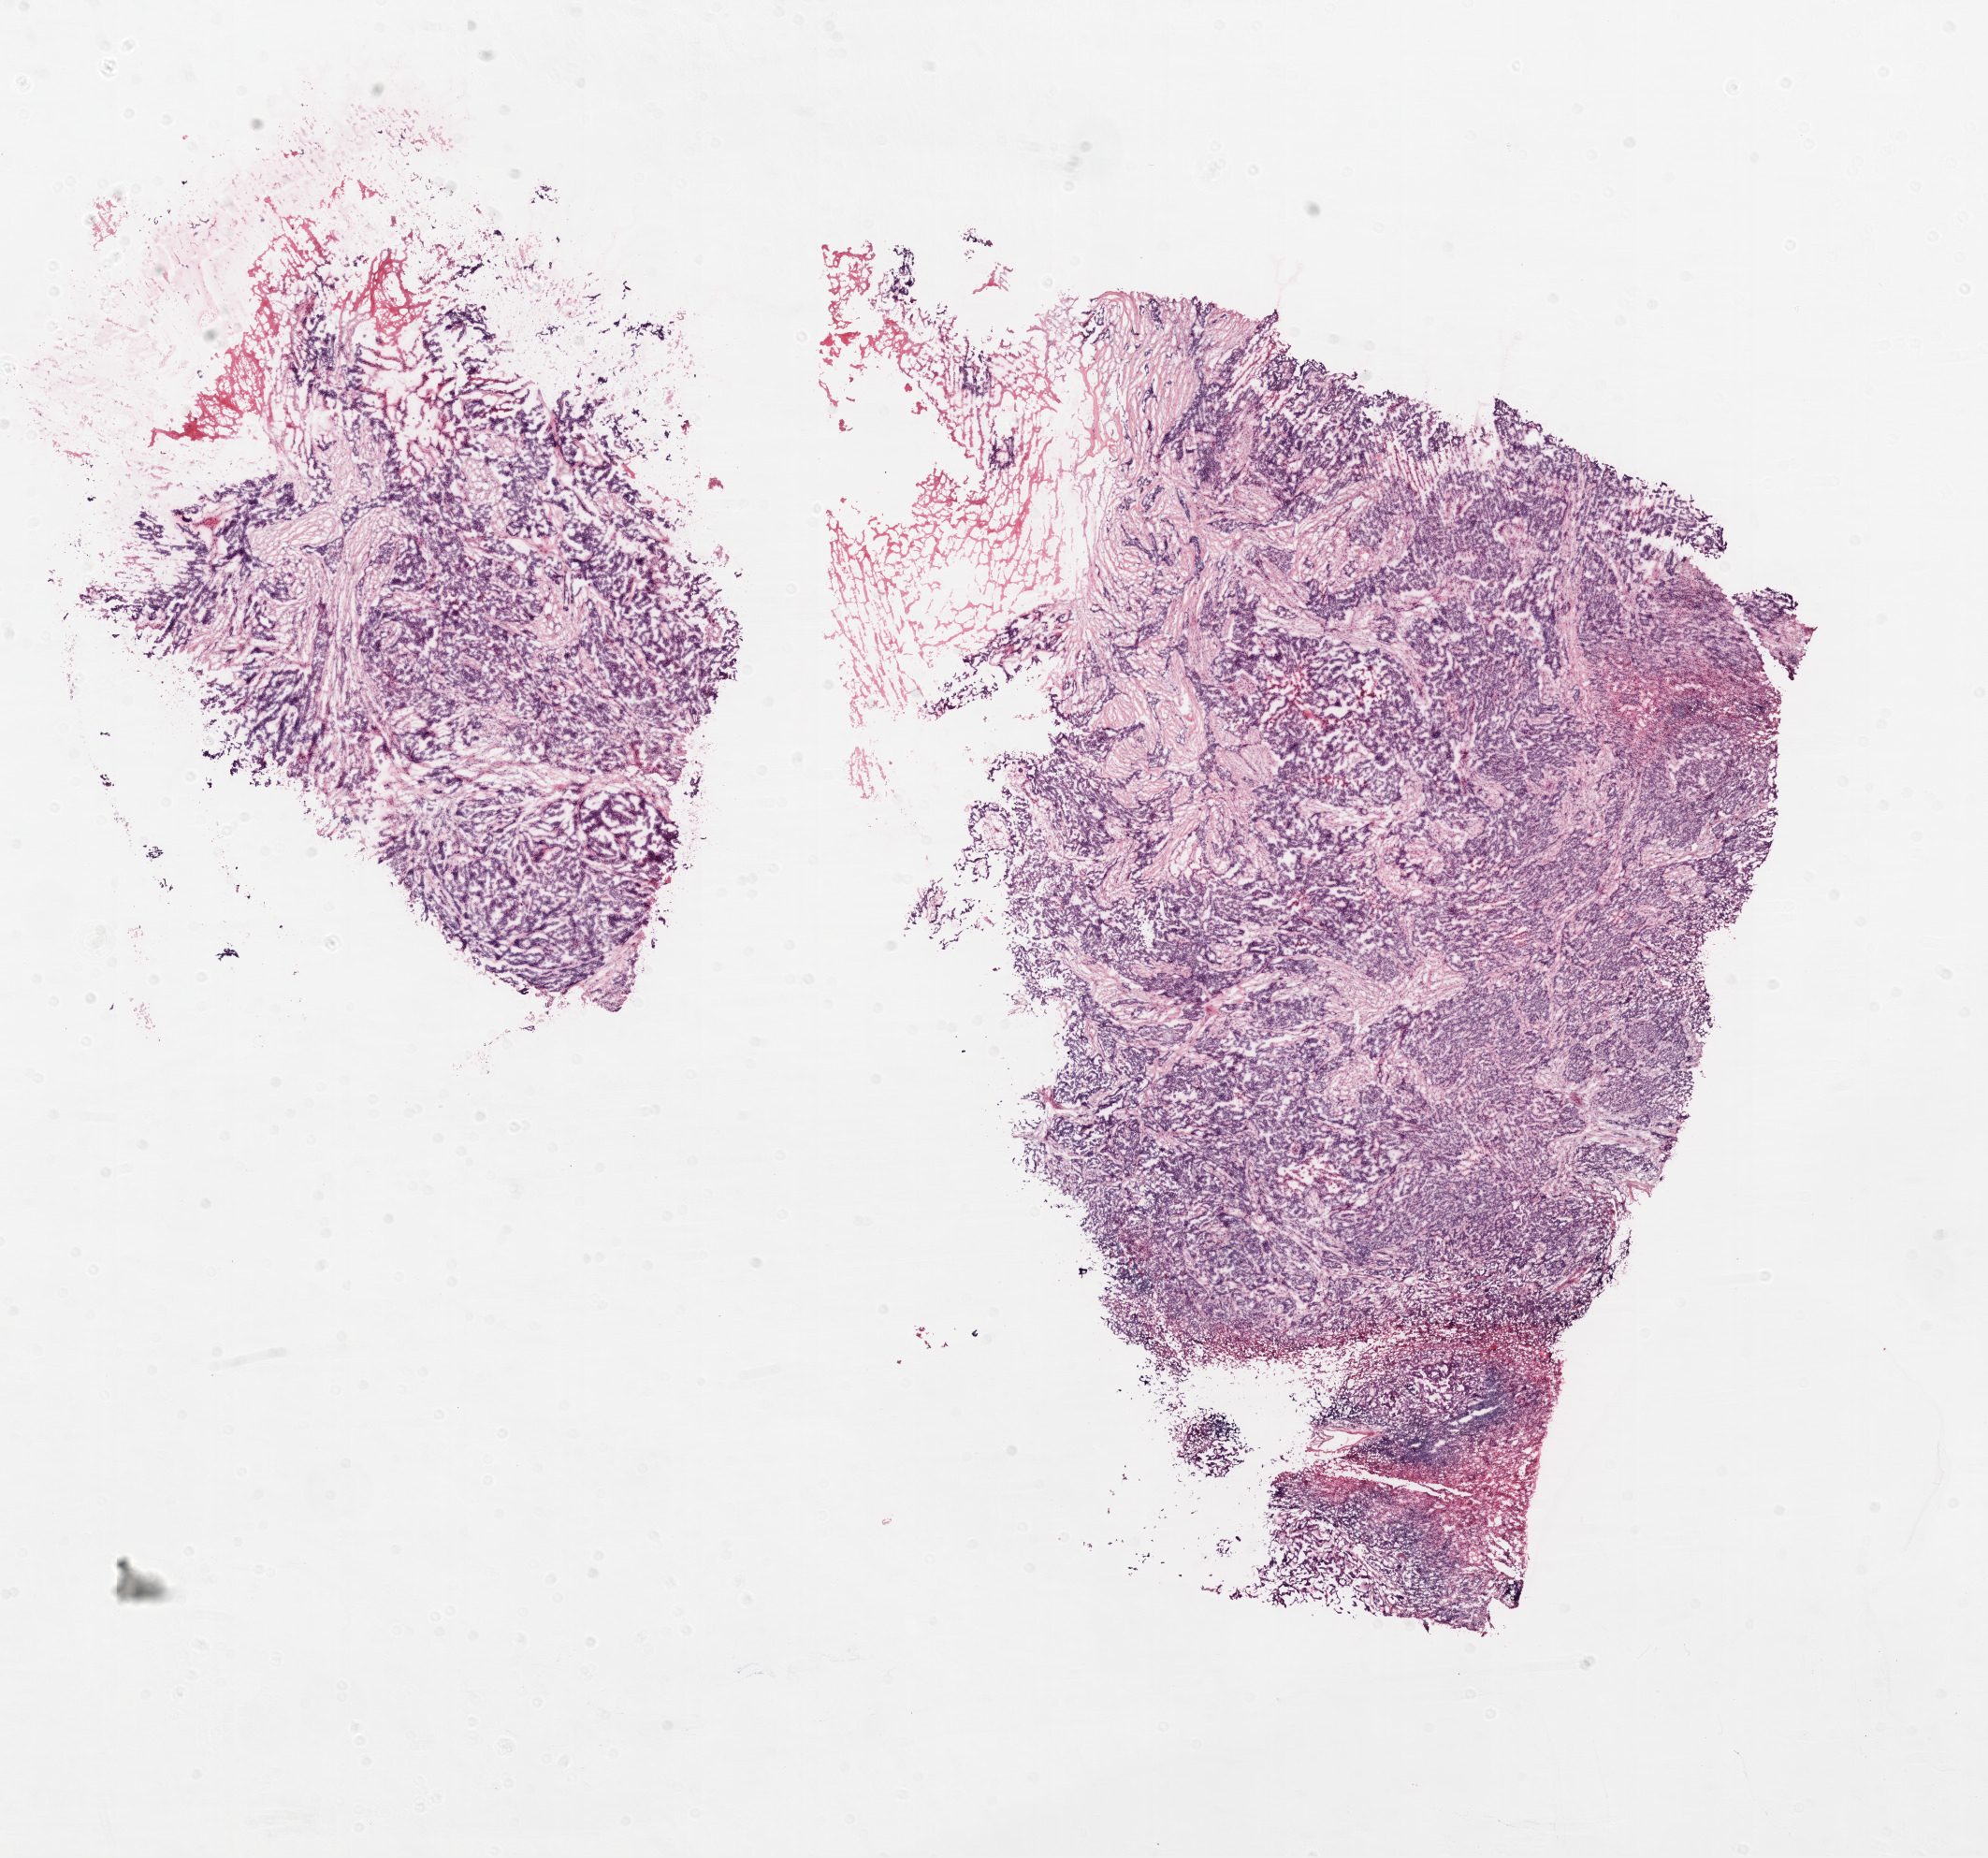
Hematoxylin and eosin (H&E) stained whole-slide image — low-resolution overview of the scanned area, about 17.1 x 15.9 mm (slide scanned at 20x). Frozen section. Sample: recurrent tumour, ovary. Patient: female, age at initial diagnosis 53 years.
This section: recurrent tumour. Patient diagnosis: Serous cystadenocarcinoma, NOS.